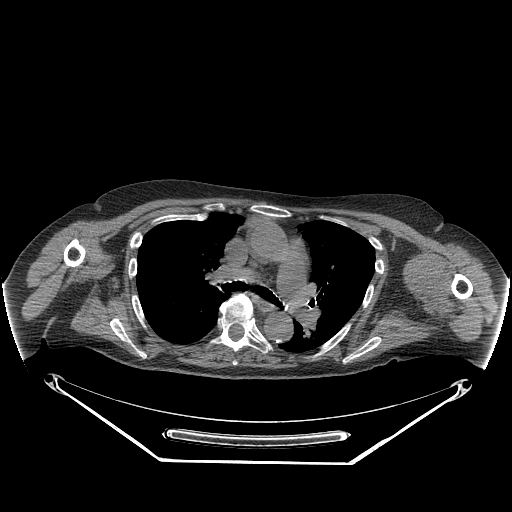
CT of an extremity soft-tissue mass (from a PET/CT study), one axial slice. Position 183 of 267 along the scan axis. 140 kVp. Soft-tissue window (W 400 / L 40 HU). 512 × 512 image matrix. Female patient. Case-level facts recorded for this patient, not image findings: histological type: pleiomorphic leiomyosarcoma; grade: high; site of the primary tumour: left biceps.
Outlined on this slice (expert contour drawn on MRI and transferred to this co-registered scan by the dataset authors):
- gross tumour volume including surrounding oedema: bounding box (x1, y1, x2, y2) in pixels: (411, 253, 448, 307)
- gross tumour volume (mass): (409, 256, 444, 295)